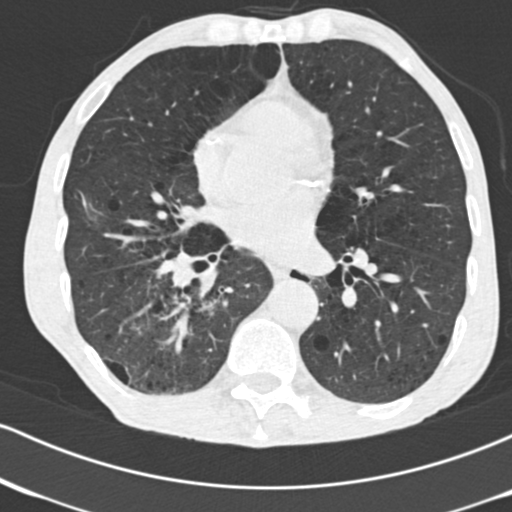
Low-dose screening chest CT, axial slice; second screening round (one year after baseline); lung window (W 1500 / L -600 HU). Male participant, aged 64 years at enrolment.
- Expert reader's lesion annotation, box from (x=123, y=224) to (x=243, y=339) px.
- Screening reader's record for this exam (one nodule recorded; not confirmed to be the boxed lesion): non-calcified nodule or mass ≥4 mm, 52 × 37 mm, spiculated (stellate) margins, soft tissue attenuation, pre-existing on the prior screen: no.